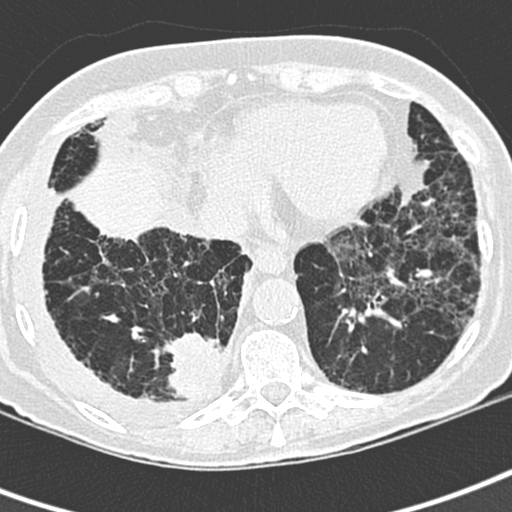
Low-dose screening chest CT, one axial slice. Position 80 of 220 along the scan axis. Lung window (W 1500 / L -600 HU). 1.3 mm slice thickness. 512 × 512 image matrix.
Annotated regions visible in this slice (expert manual segmentation):
- lesion 1 (tumor, lower lobe of right lung): bounding box <163,332,223,400> (left, top, right, bottom; pixels)